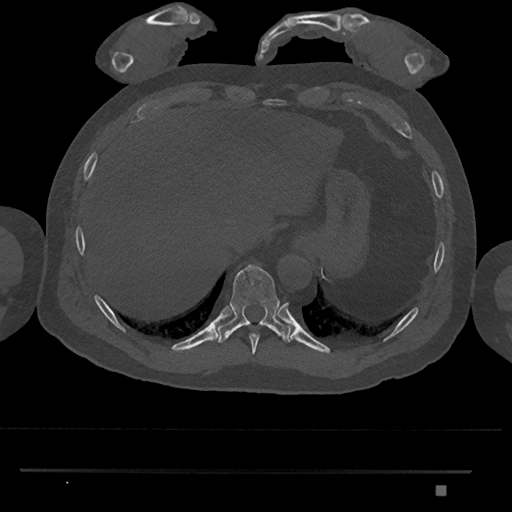
CT including the spine, one axial slice. Position 1017 of 1134 along the scan axis. Reconstruction kernel Br40s/3. 120 kVp. Bone window (W 1800 / L 400 HU). 0.5 mm slice thickness. 512 × 512 image matrix. Patient: male, 65 years. Case-level facts recorded for this patient, not image findings: primary cancer: prostate.
Annotated regions visible in this slice (semi-automatic segmentation, software-assisted and operator-edited):
- T10 vertebra: bounding box [x1, y1, x2, y2] px = [216, 264, 290, 343]
- T9 vertebra: [249, 333, 260, 355]